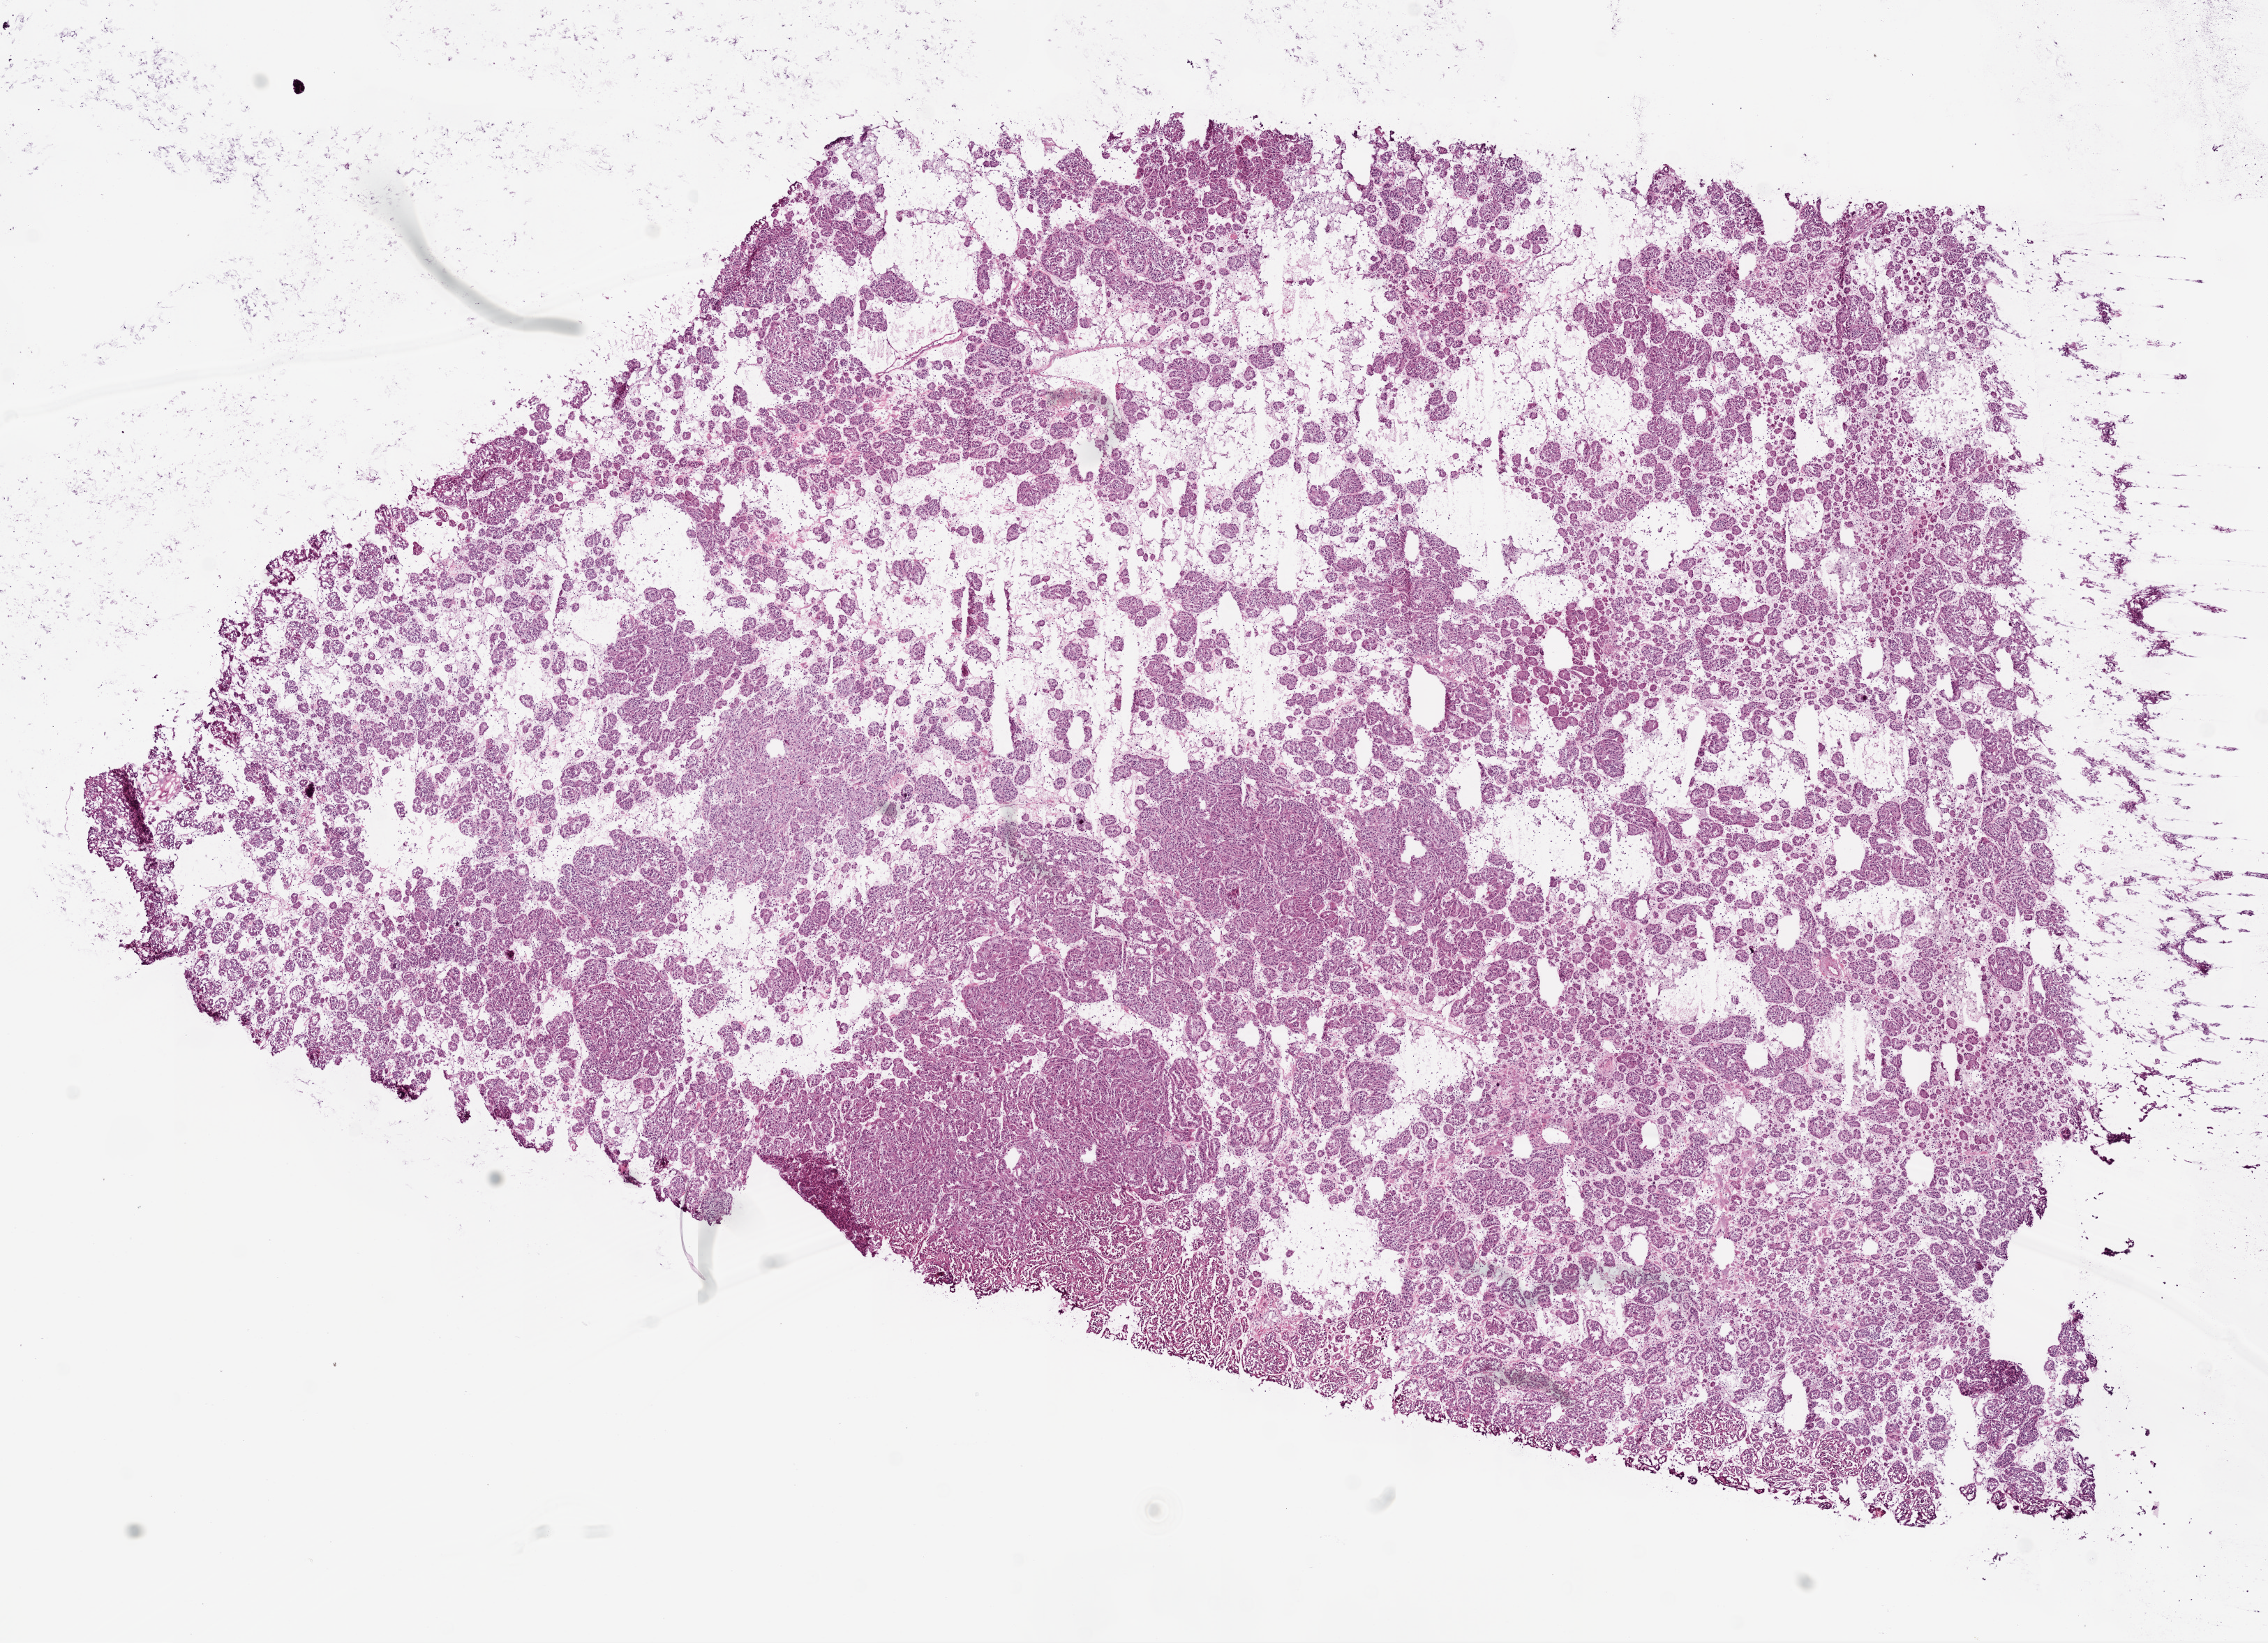
H&E-stained whole-slide image — shown as a low-resolution overview of the whole scanned area (about 13.0 x 9.4 mm); frozen section; primary tumour sample from the kidney. Patient: female, age at initial diagnosis 48 years. Composition of this section per pathologist review: tumour cells 80%, tumour nuclei 80%, normal cells 0%, stromal cells 20%, necrosis 0%.
Diagnosis: Papillary adenocarcinoma, NOS.